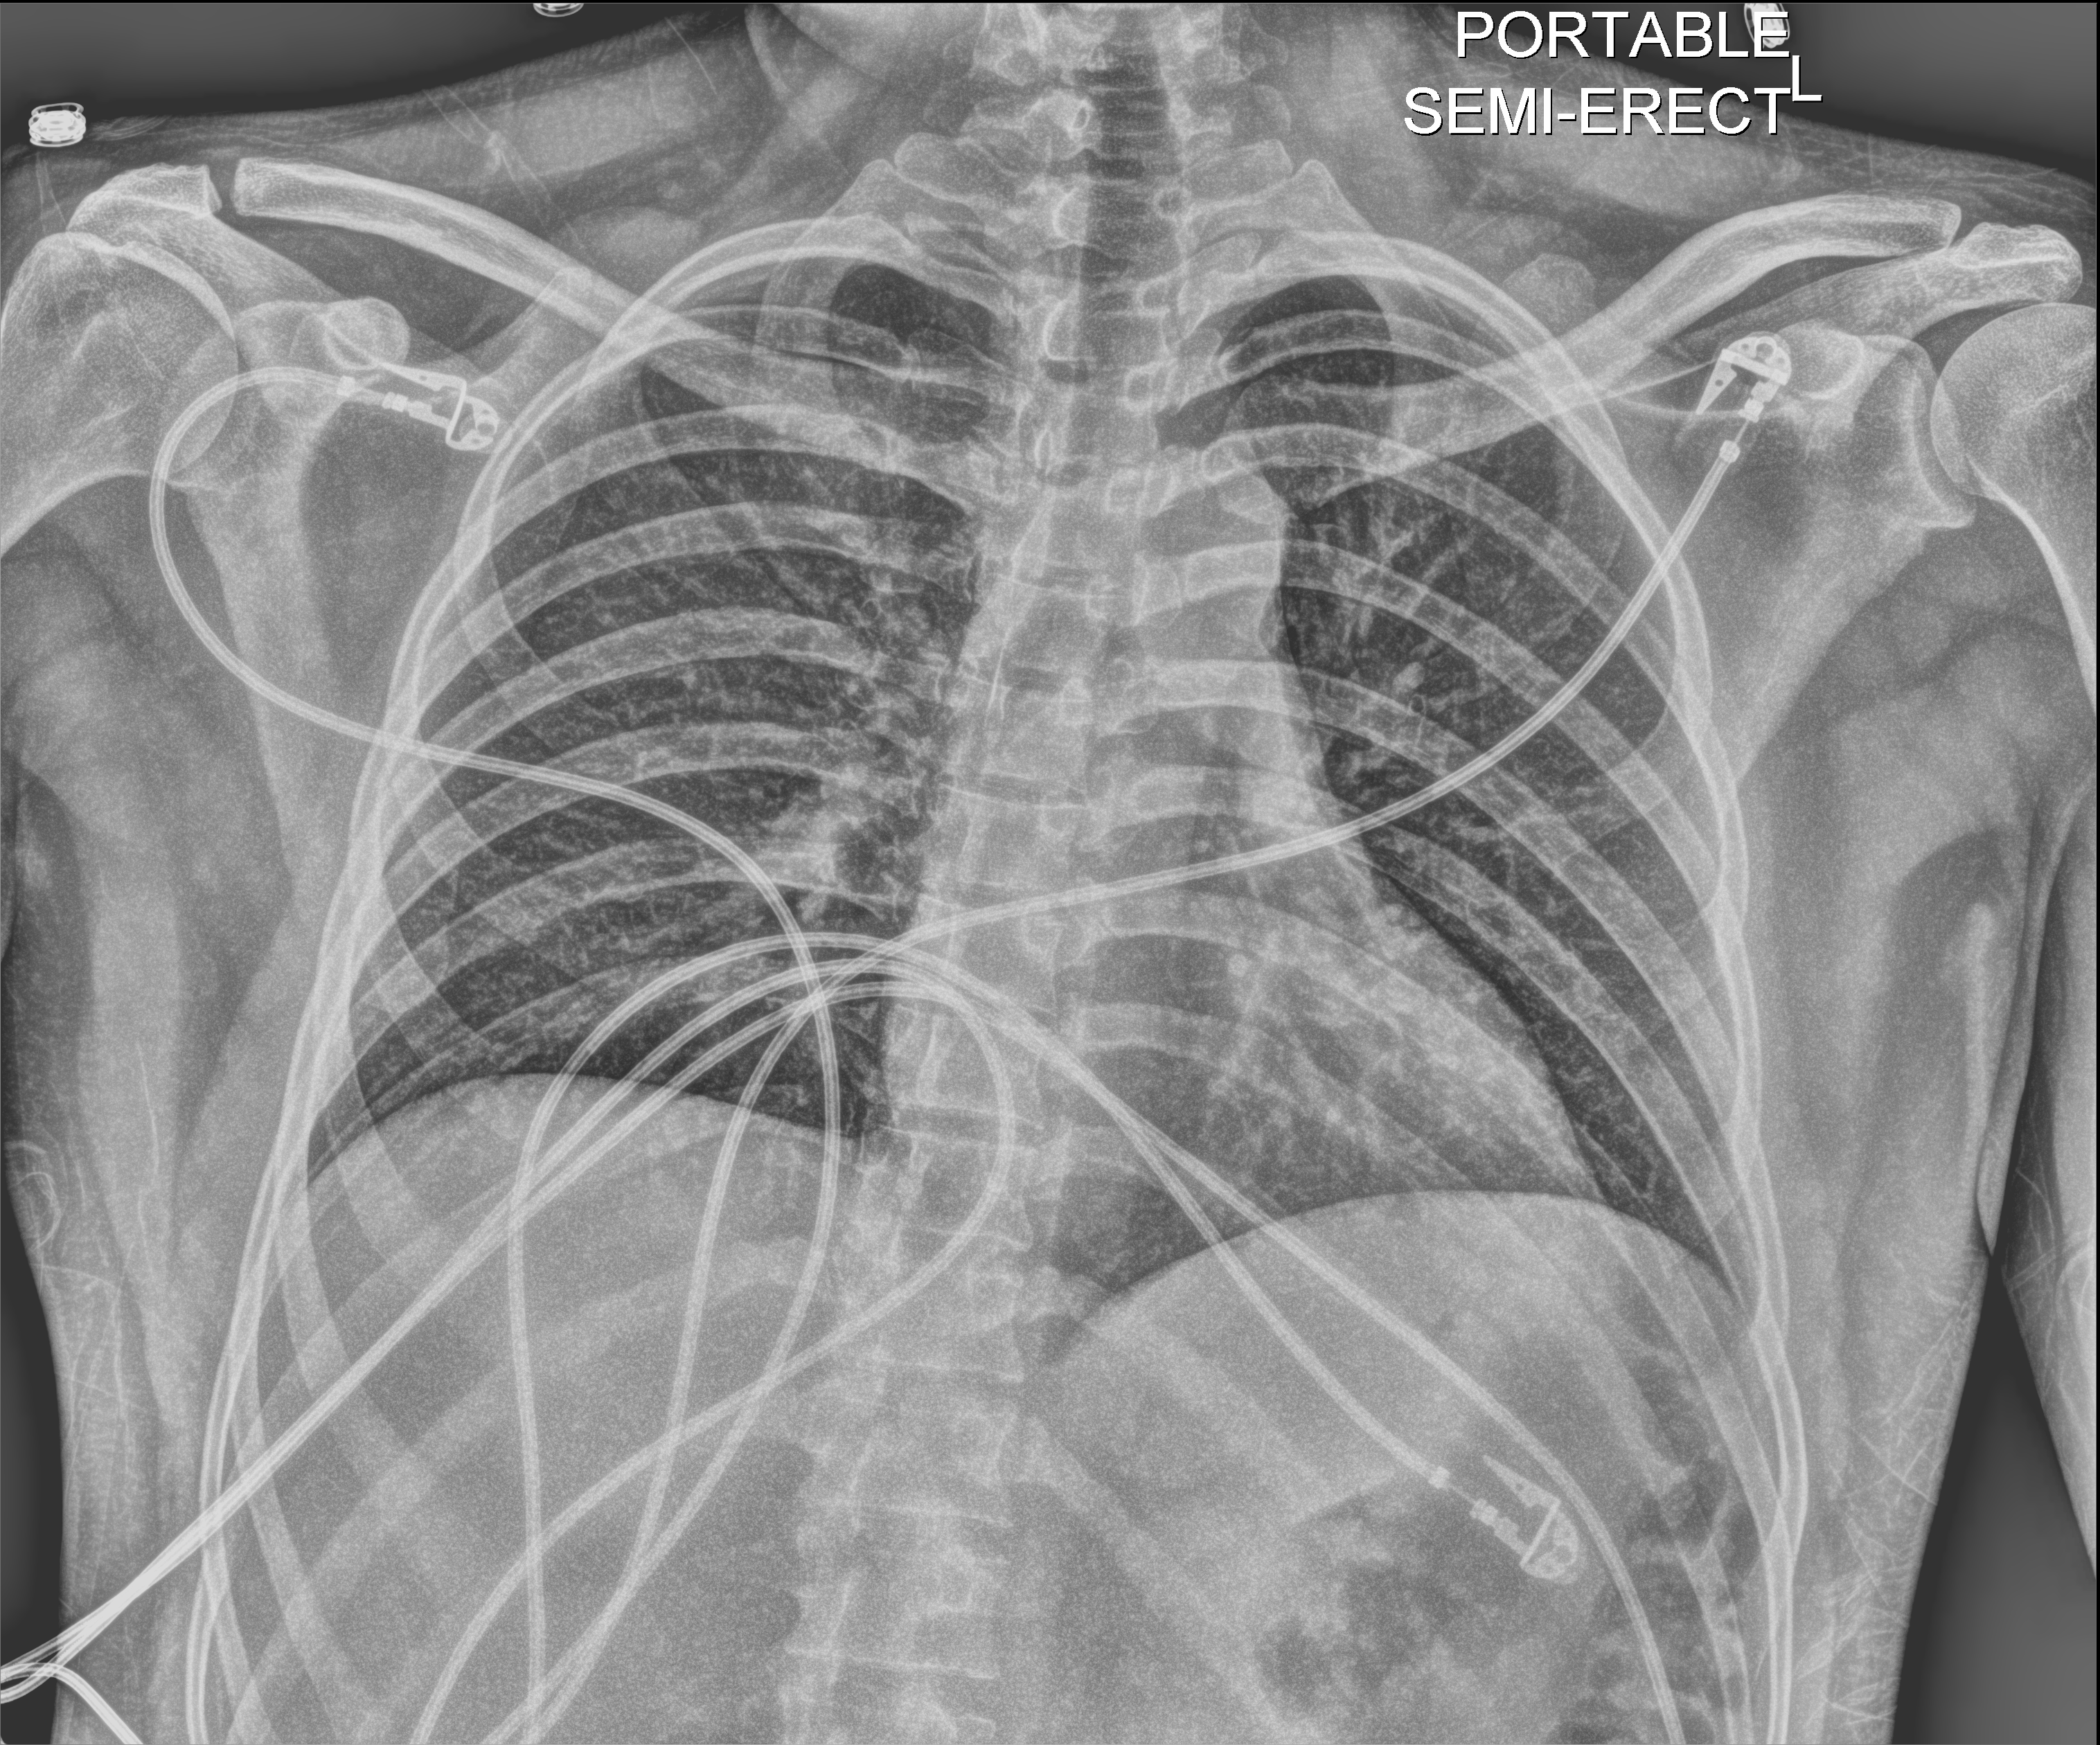
Portable chest radiograph; anteroposterior (AP) projection. Male patient hospitalised with COVID-19, age 18–59 years.
Hospital-stay facts (about this admission, not read from this image; timing relative to this image not recorded): mechanically ventilated during this hospital stay: no; length of hospital stay: 7 days; admitted to intensive care during this hospital stay: no.